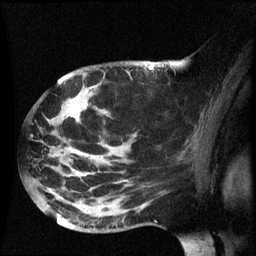
Breast MRI (dynamic contrast-enhanced), one sagittal slice. Slice 39 of 60 in the series (ordered by position). Dynamic contrast-enhanced series, image 2 of 3 at this slice position (ordered by acquisition). 1.5 T. TE 4.2 ms, TR 8.4 ms. 2.5 mm slice thickness. 256 × 256 image matrix, field of view 220 × 220 mm. Patient: female, 49 years.
Structures marked on this image (semi-automatic segmentation, software-assisted and operator-edited):
- analysis volume of interest (the breast-tissue region the enhancement analysis was run in; not a lesion): bounding box (x1, y1, x2, y2) in pixels: (27, 72, 157, 233)
- tumour enhancement mask (voxels above the 70 % enhancement threshold inside the analysis volume of interest): (71, 112, 79, 121)